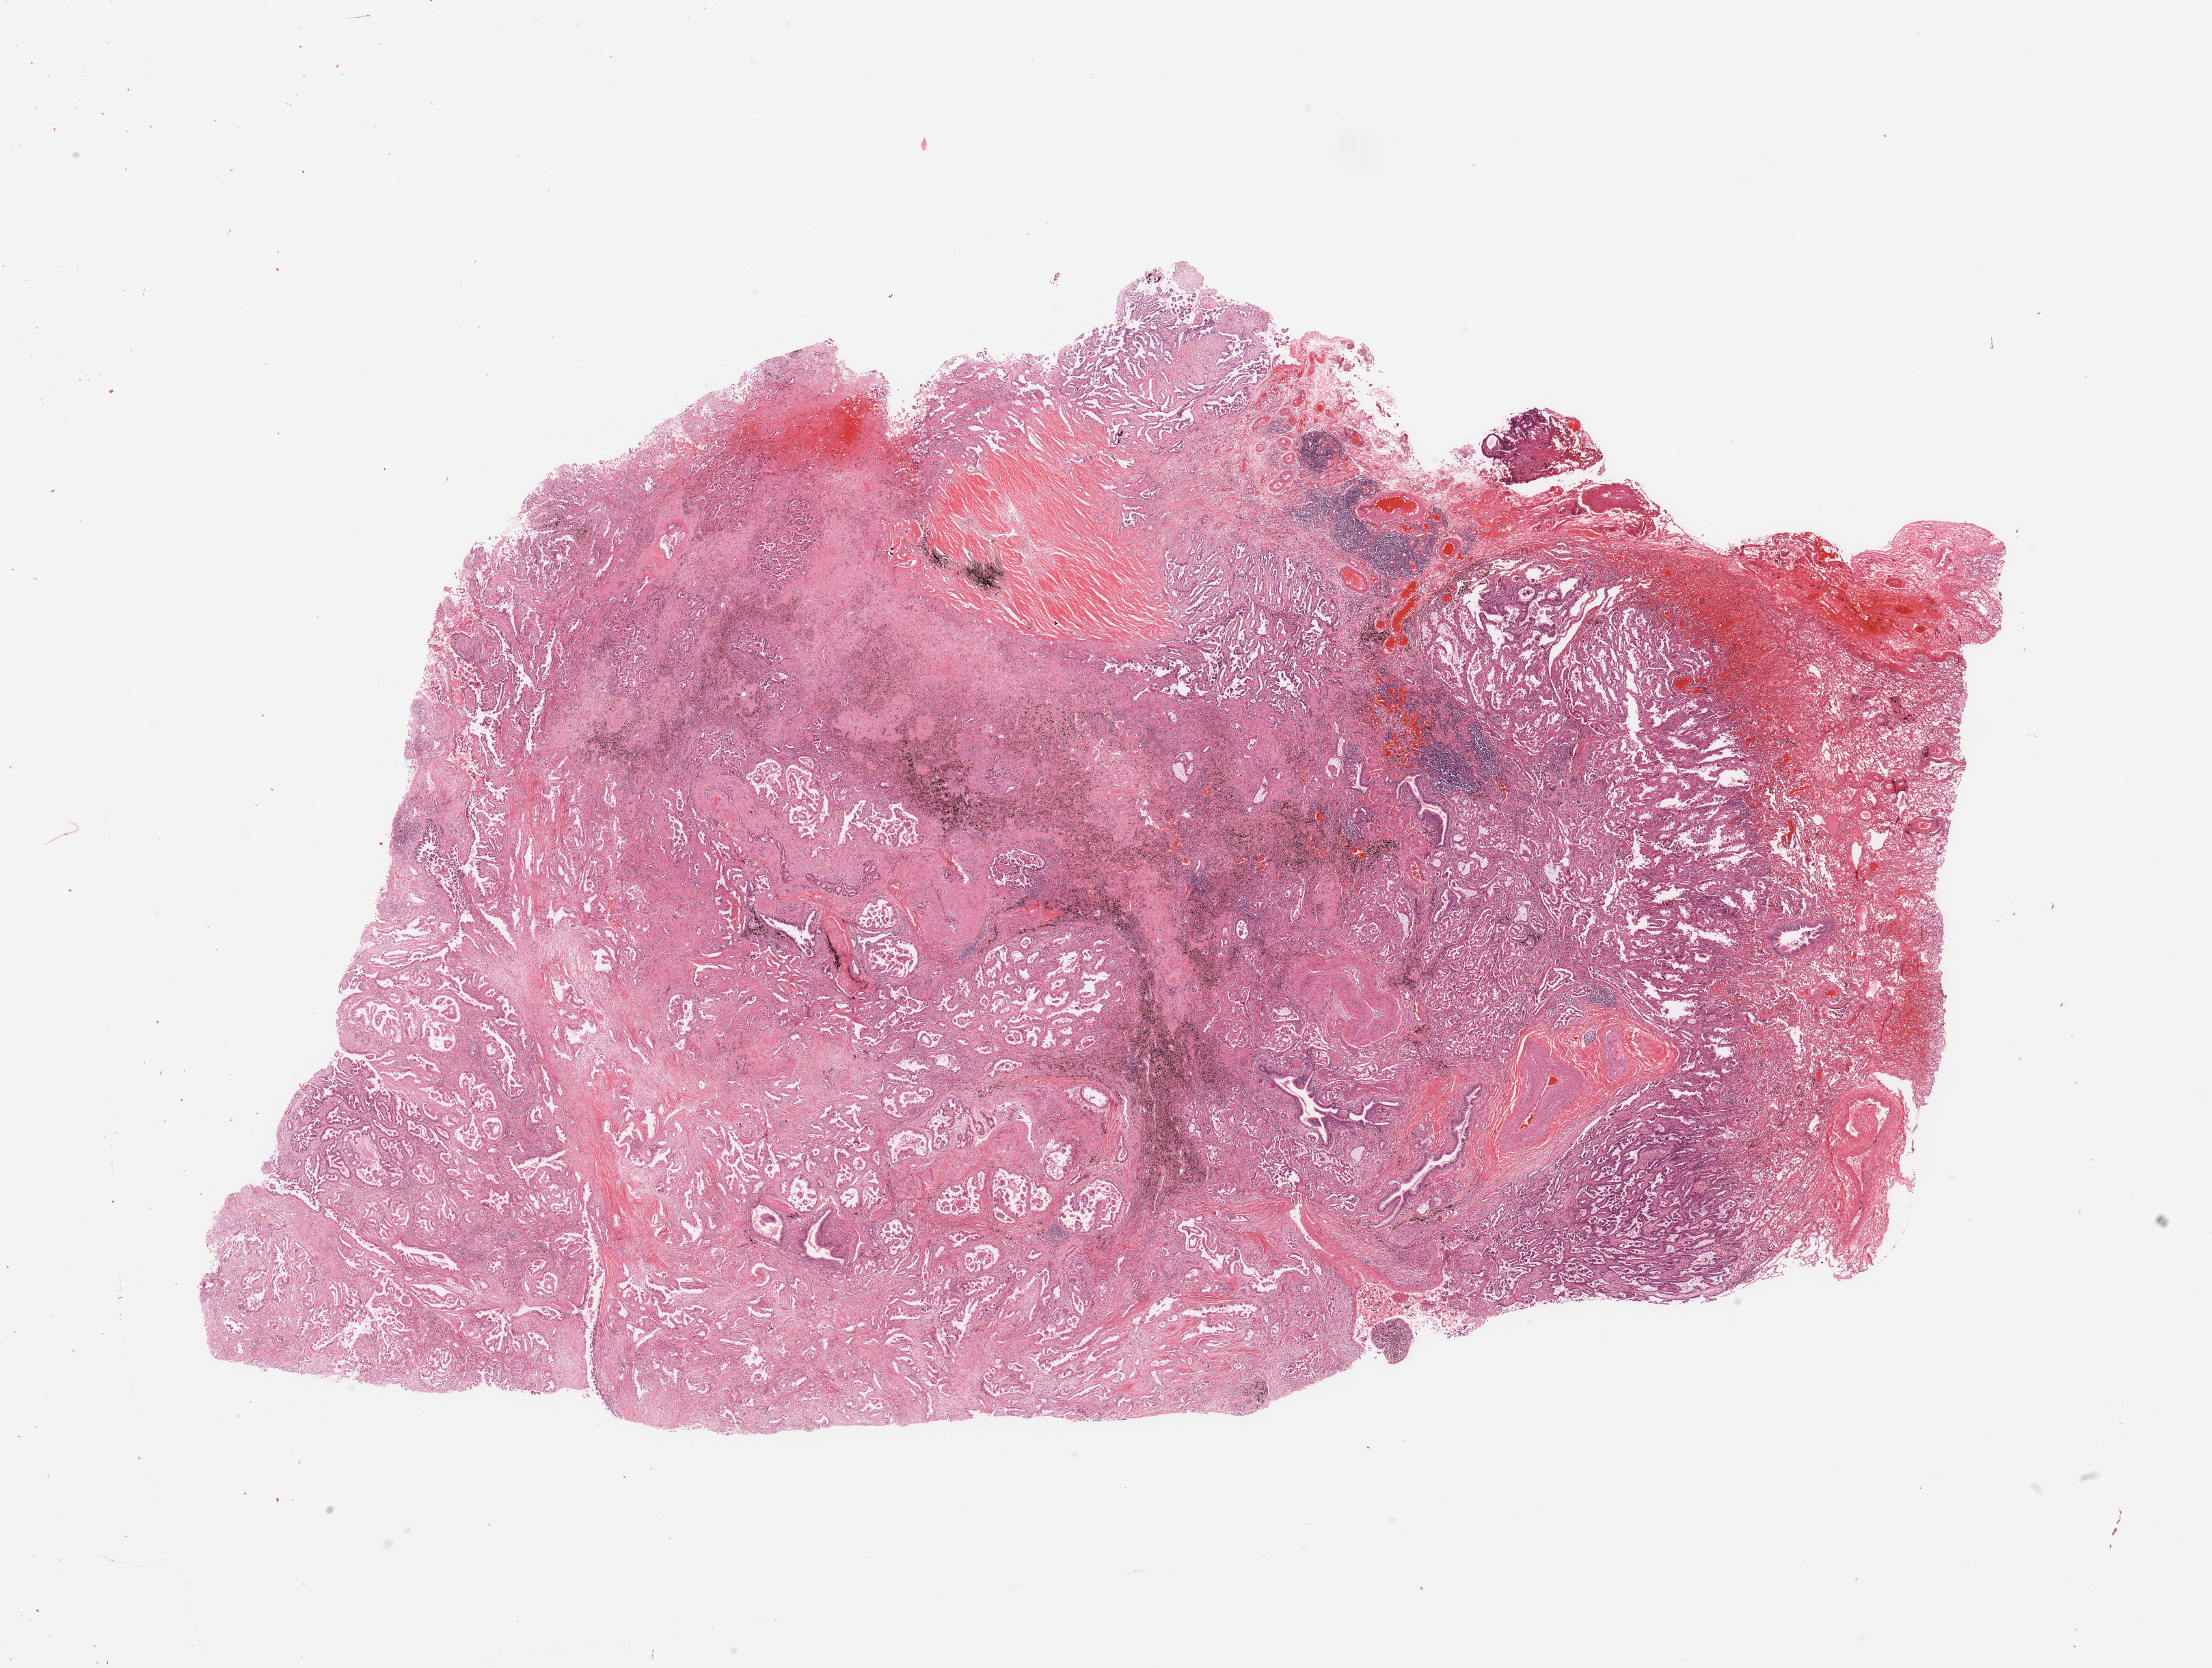
Digitized H&E tissue section (whole slide), whole scanned area (about 25.6 x 19.3 mm, slide scanned at 20x) shown as a low-resolution overview, tumour tissue sample, lung. Patient: female, age 60 years. Histologic grade: G2 (moderately differentiated).
Histologic diagnosis: Adenocarcinoma, NOS. AJCC pathologic stage: IB.